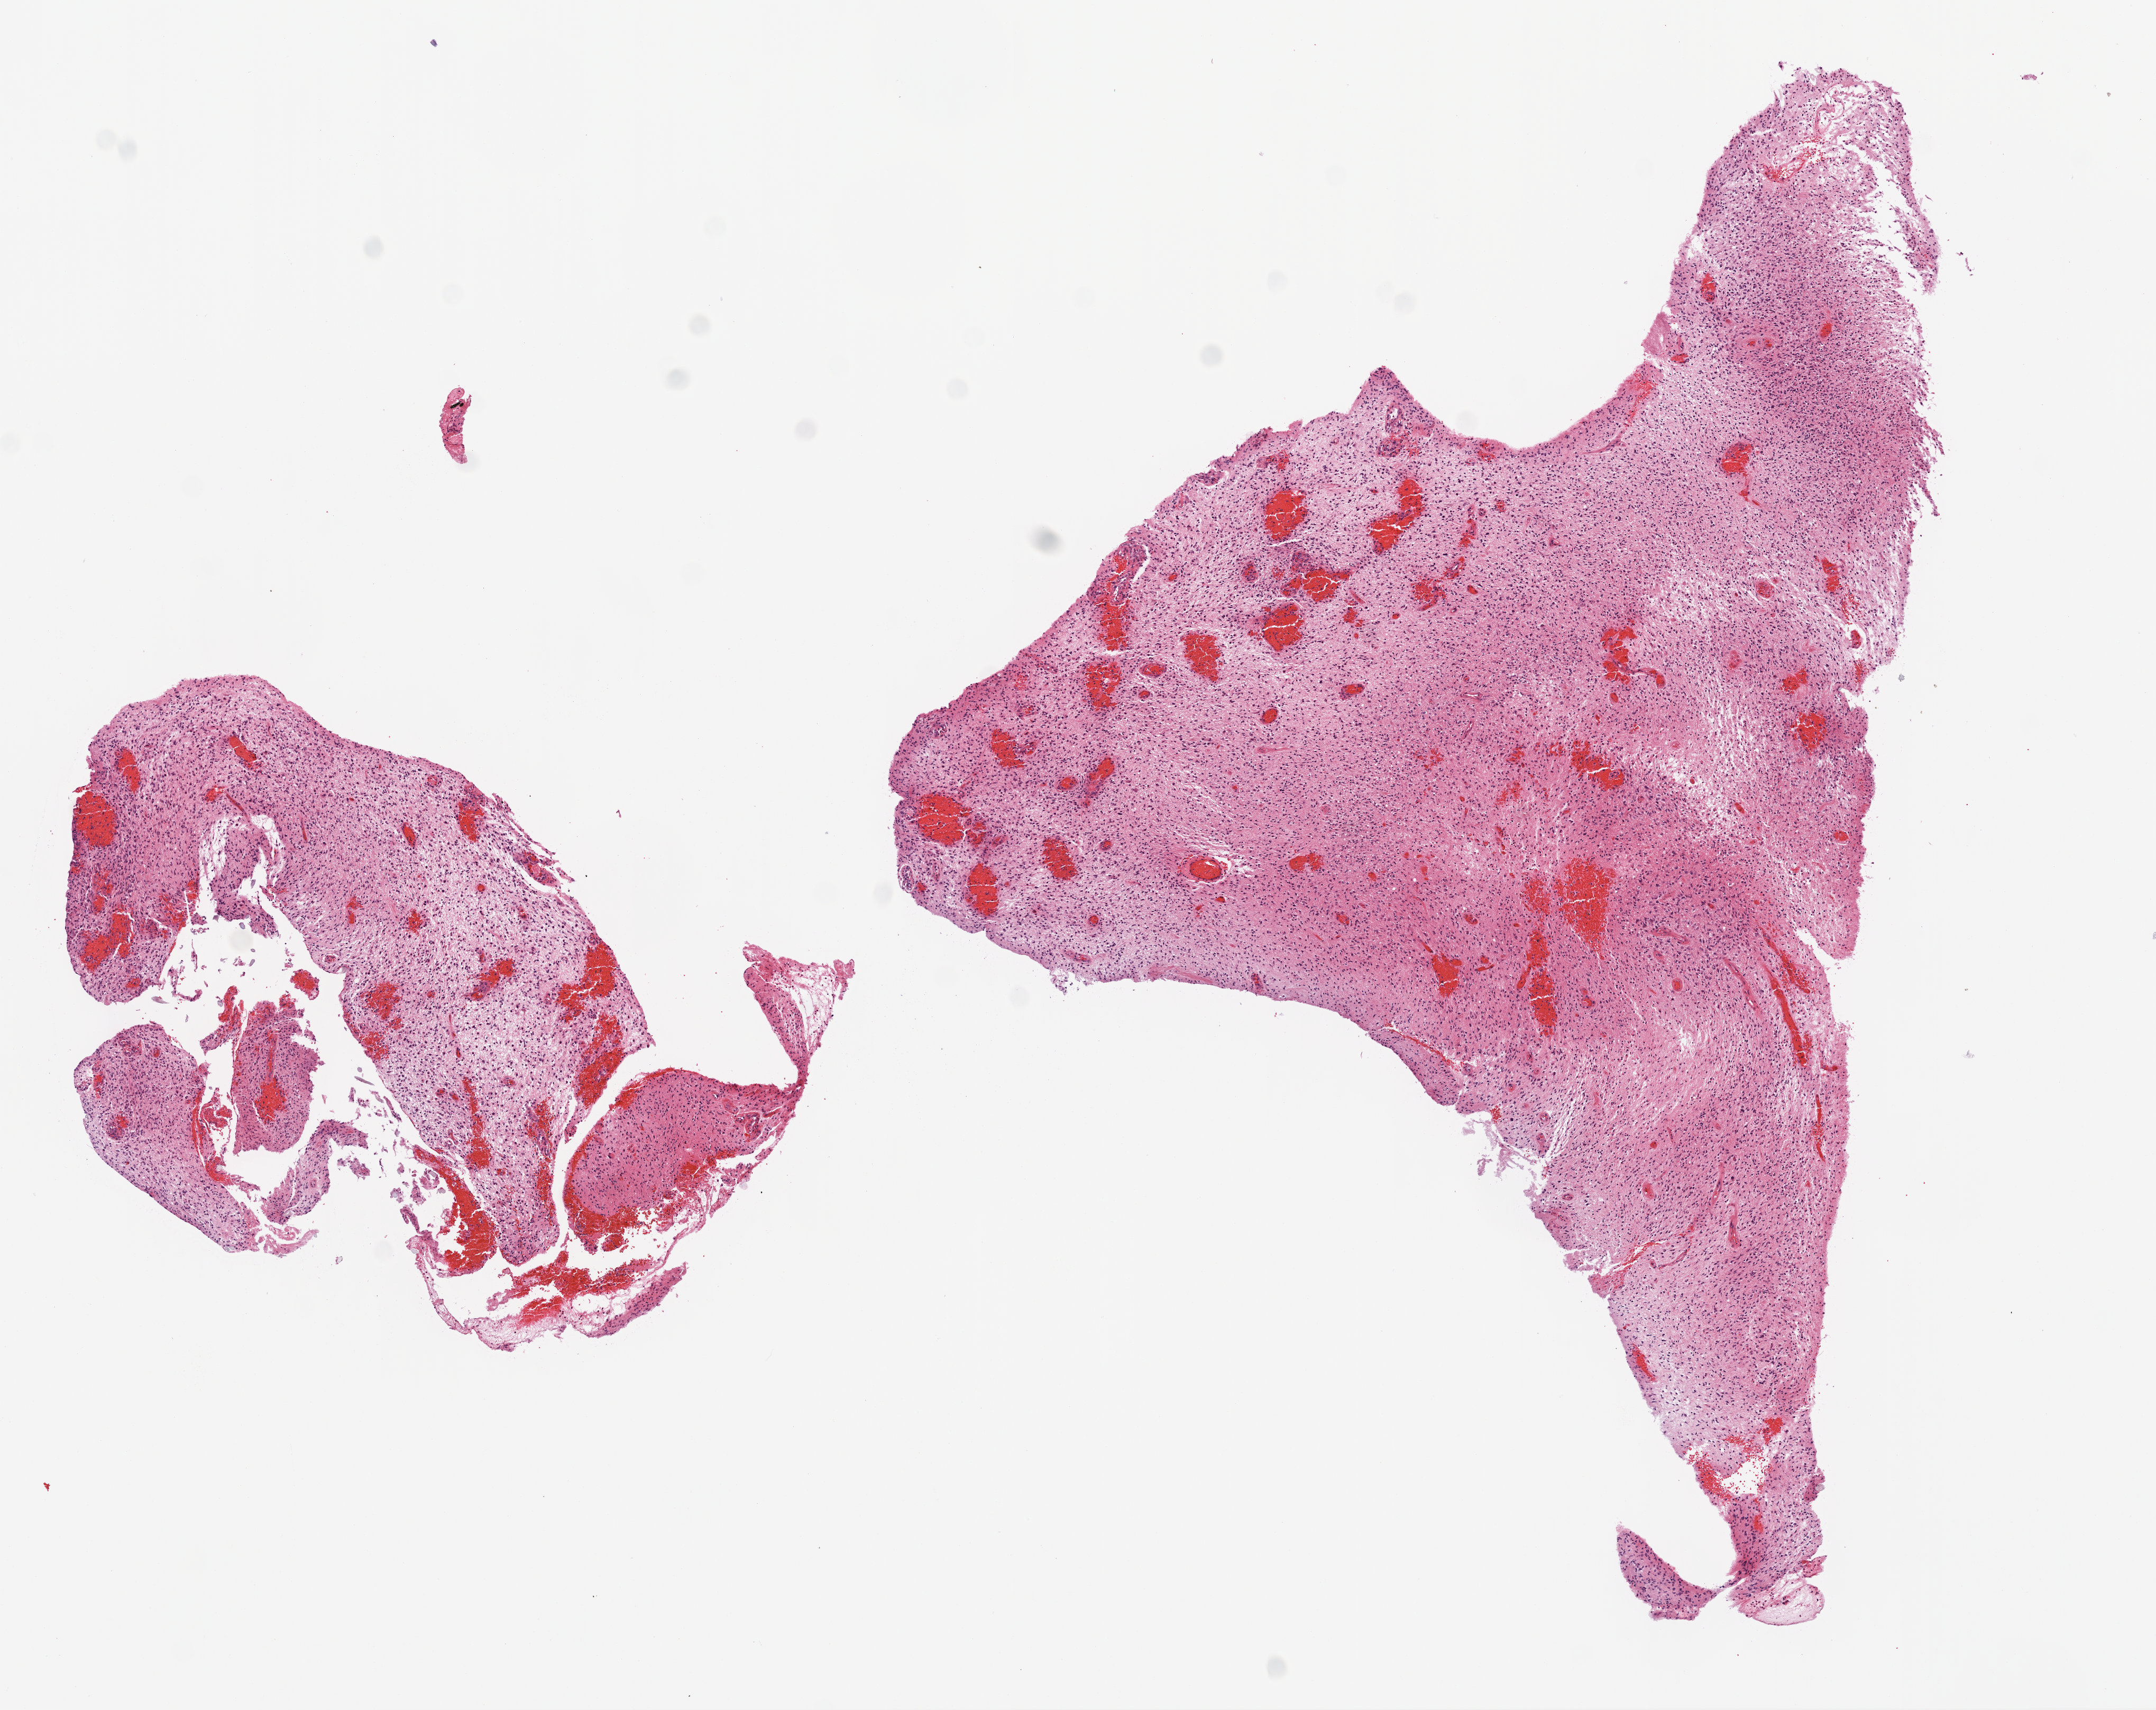
Digitized H&E-stained tissue section (whole slide), whole scanned area (about 8.2 x 6.5 mm) shown as a low-resolution overview; formalin-fixed paraffin-embedded (FFPE) diagnostic section; sample: primary tumour, brain. Male patient; age at initial diagnosis 73 years.
Pathologic diagnosis: Glioblastoma.